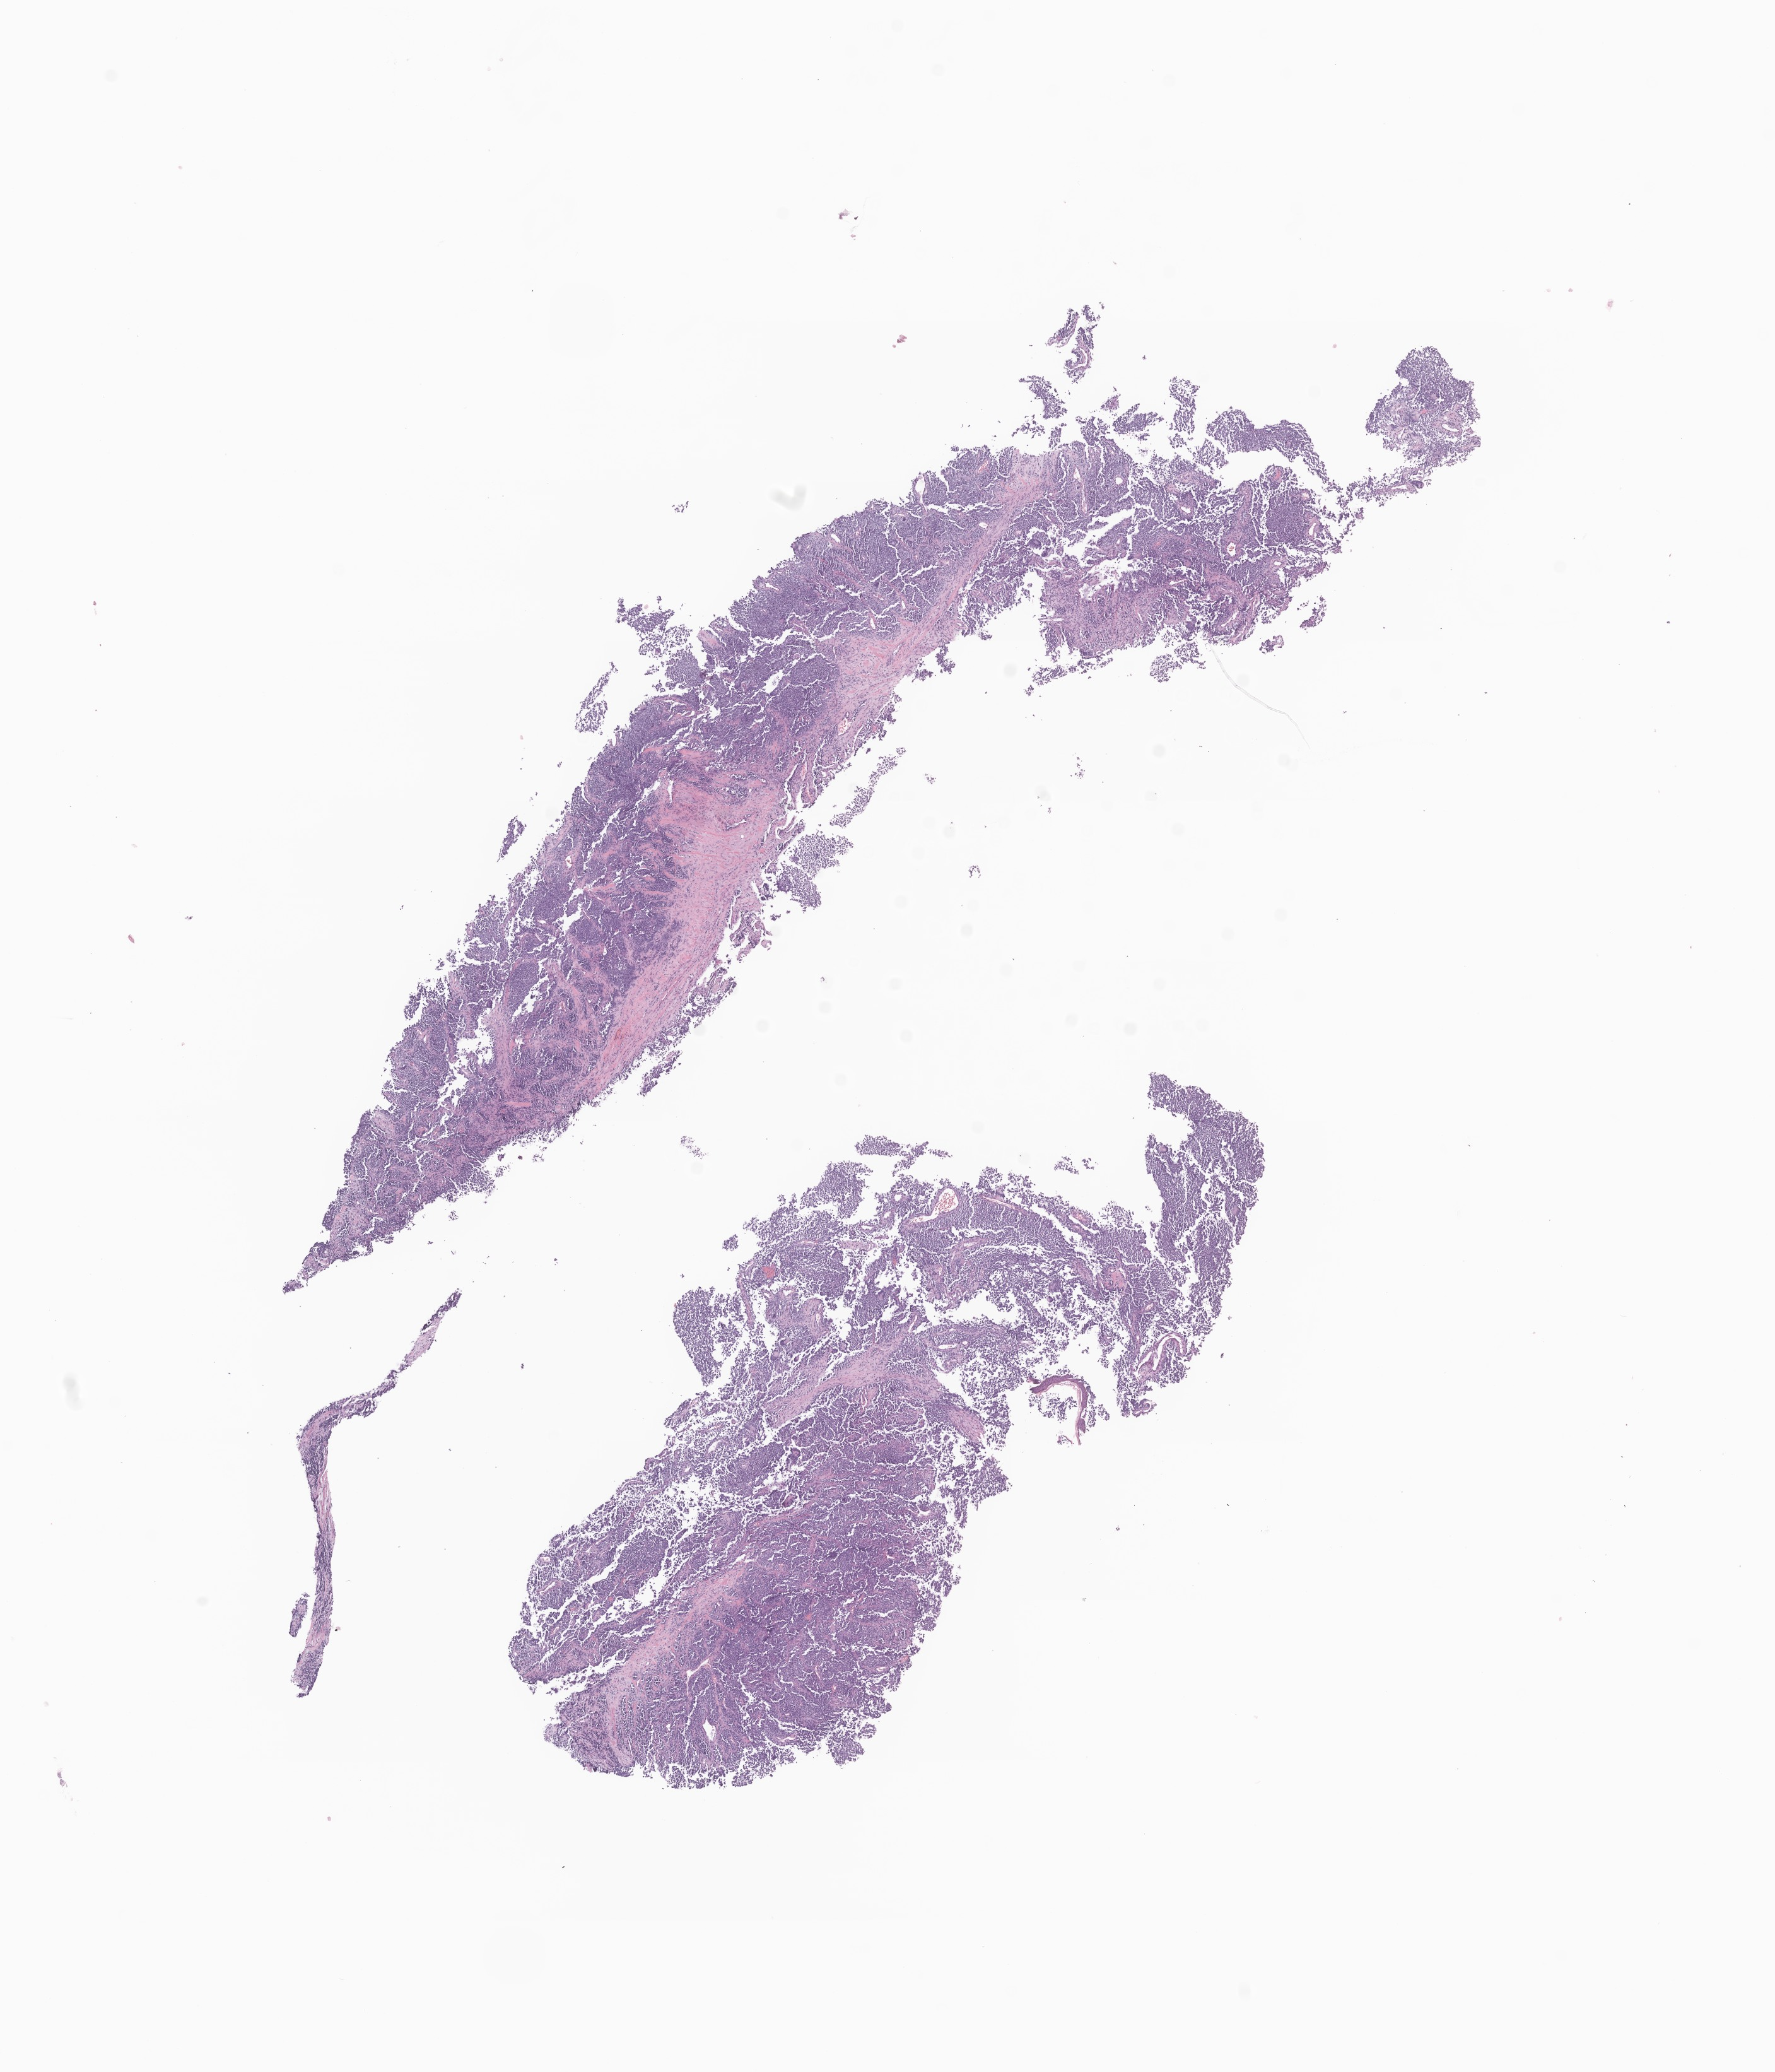
Whole-slide image, hematoxylin and eosin (H&E) stain of tumor tissue from the head and neck, low-resolution overview of the scanned area, about 11.9 x 13.8 mm. Formalin-fixed, paraffin-embedded (FFPE) tissue. Male patient, age 116 months.
Diagnosis: Rhabdomyosarcoma, NOS.